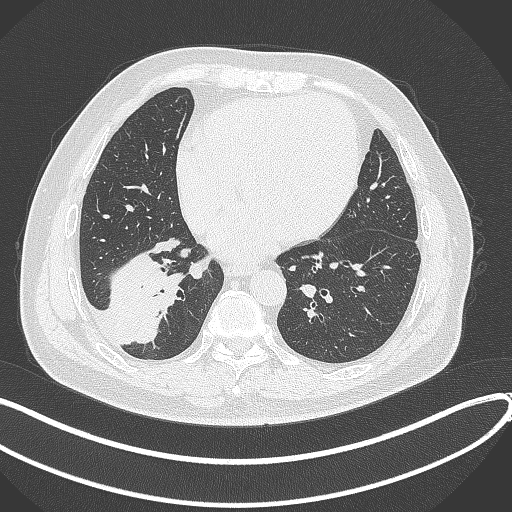
Chest CT, one axial slice; position 127 of 360 along the scan axis; 120 kVp; lung window (W 1500 / L -600 HU); 1 mm slice thickness; 512 × 512 image matrix, field of view 400 × 400 mm. Patient: male, 59 years.
Structures marked on this image (rectangle marked by the reading radiologist):
- lung tumour (recorded histology: adenocarcinoma): box from (x=106, y=250) to (x=186, y=346) px